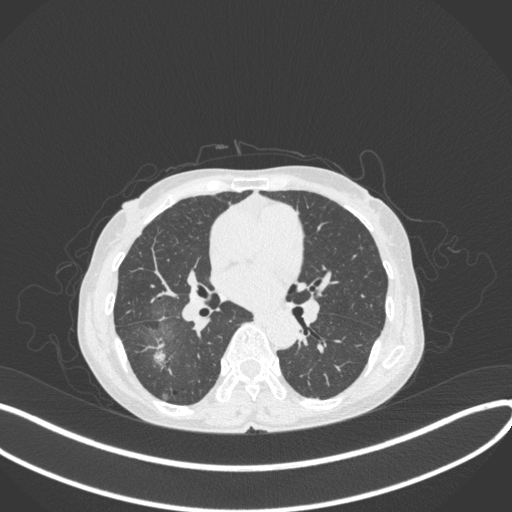
Chest CT, one axial slice; slice 203 of 379 in the series (ordered by position); lung window (W 1500 / L -600 HU); 1 mm slice thickness; 512 × 512 image matrix, field of view 400 × 400 mm. Female patient, age 69 years. Case-level facts recorded for this patient, not image findings: clinical TNM (as recorded): T1b N0 M0.
Structures marked on this image (rectangle marked by the reading radiologist):
- lung tumour (recorded histology: adenocarcinoma): bounding box <145,336,173,373> (left, top, right, bottom; pixels)